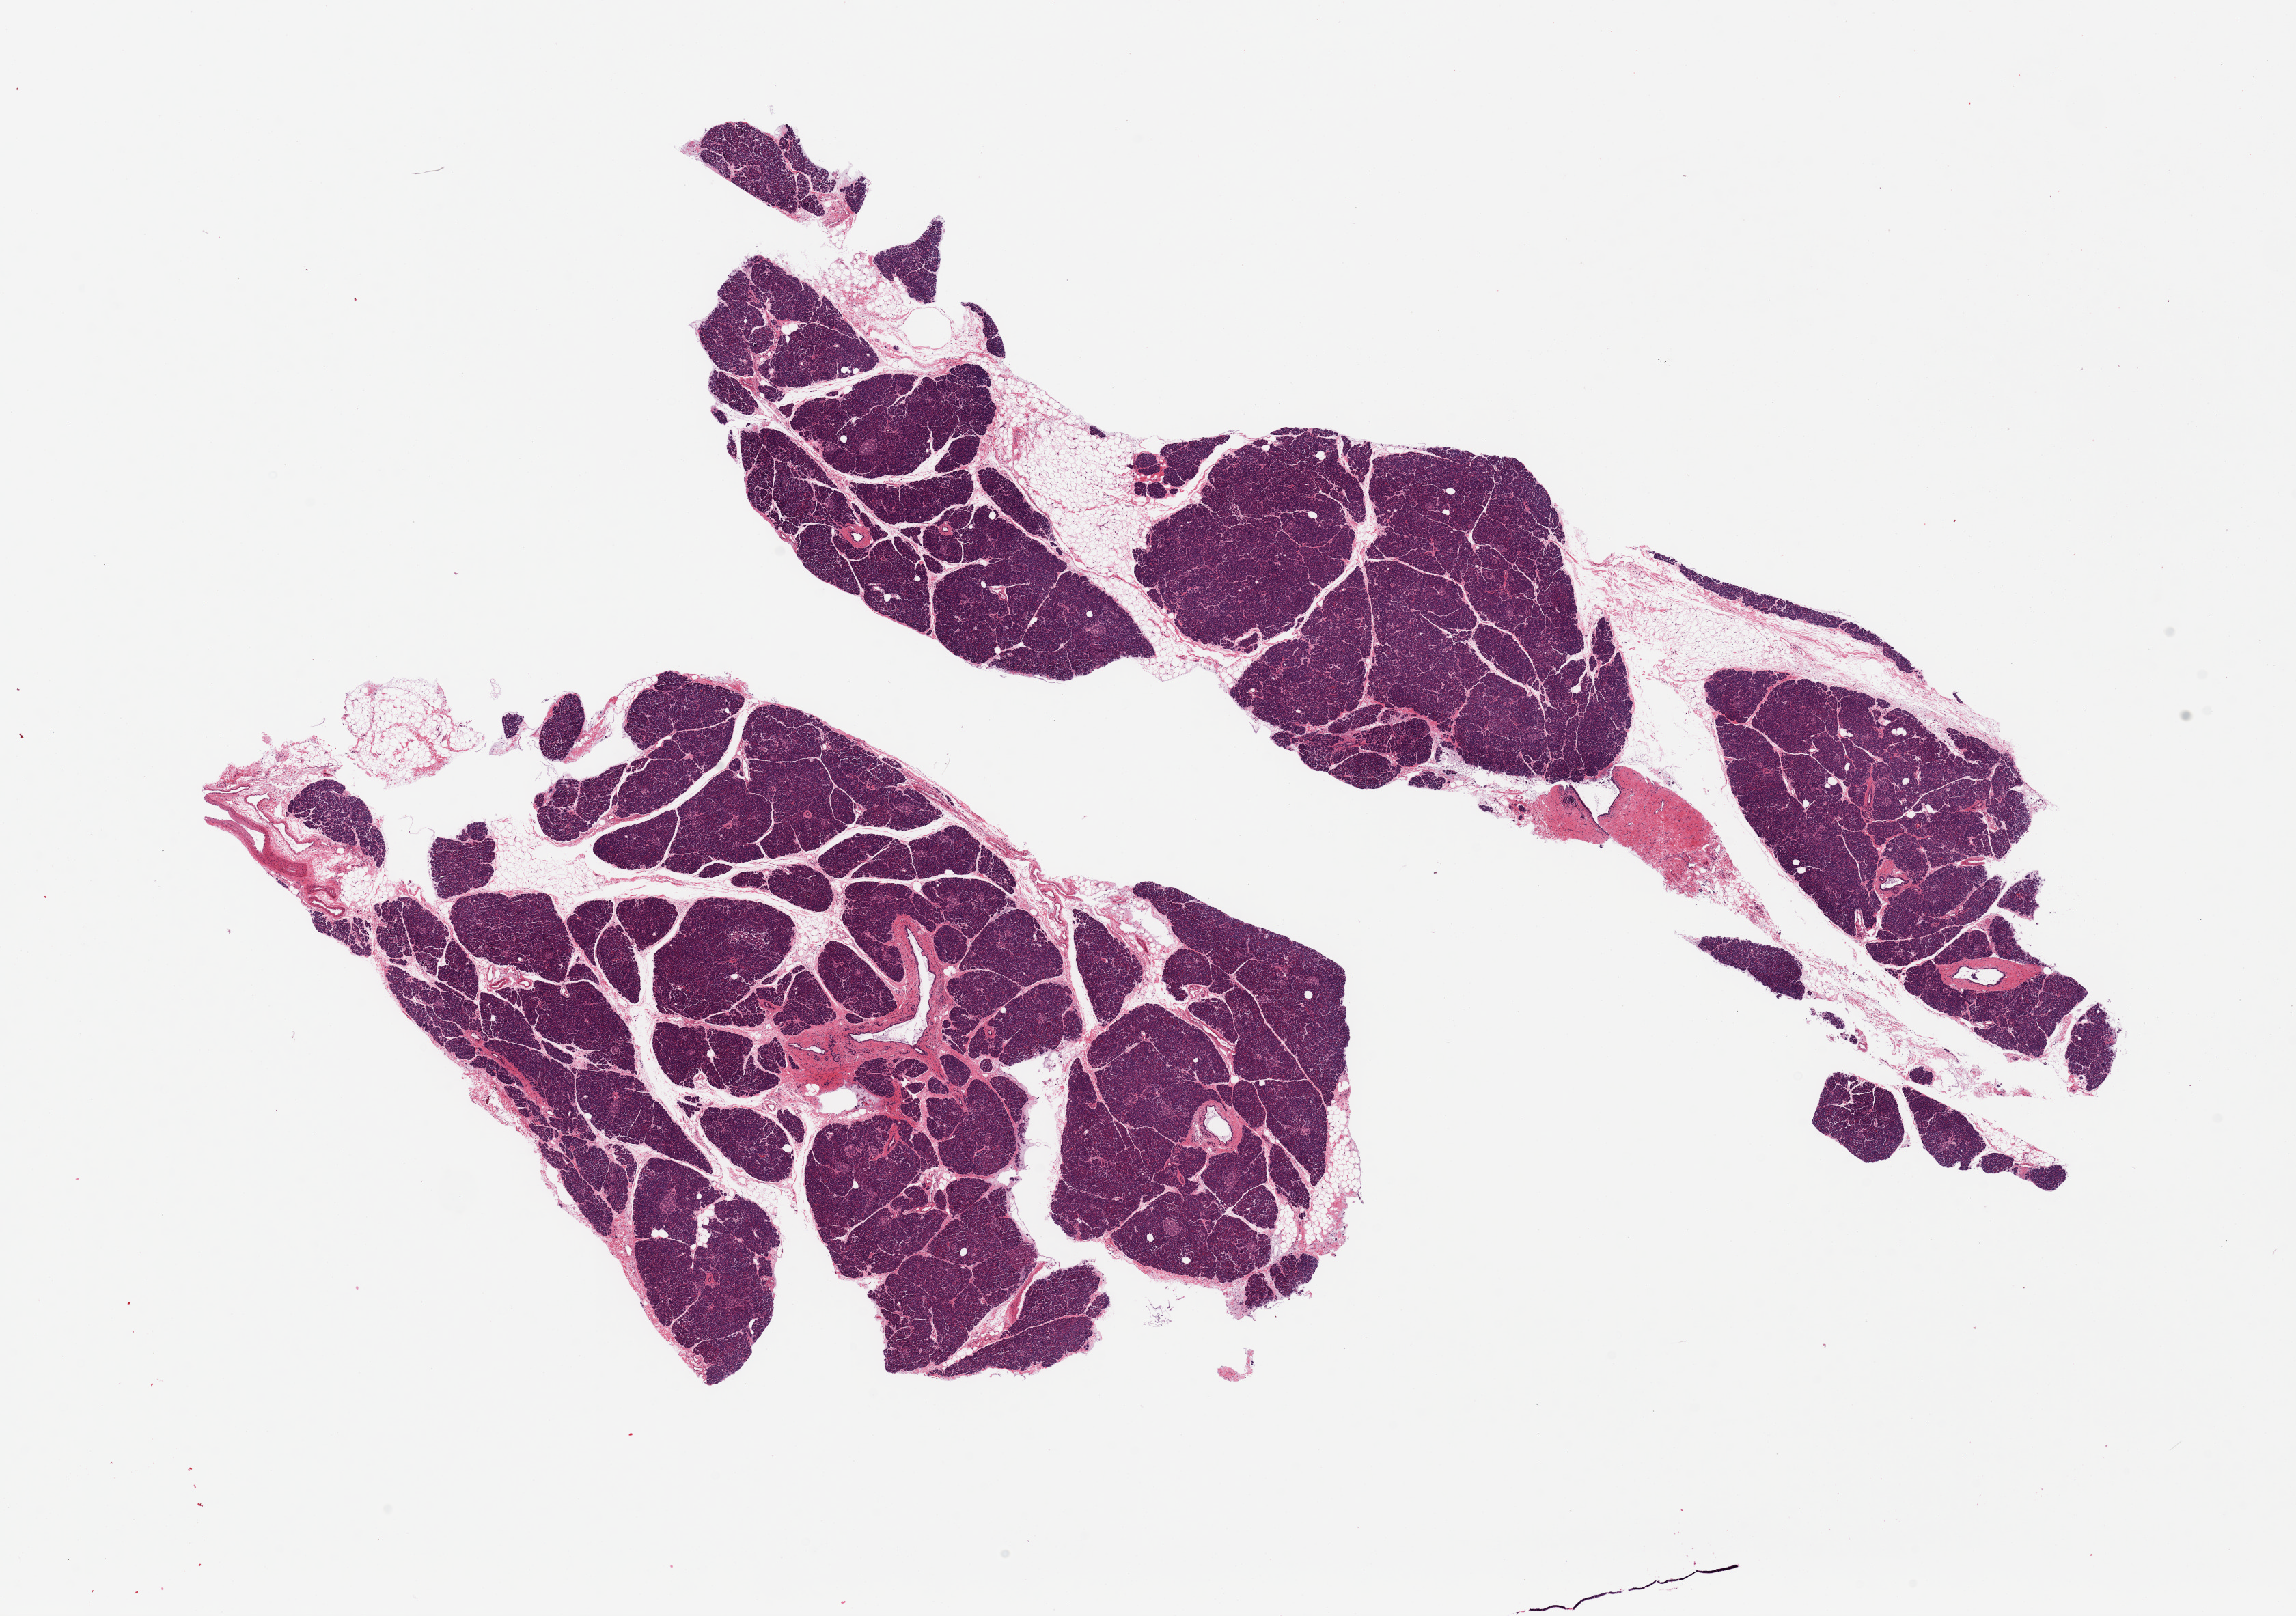
Digitized hematoxylin and eosin (H&E)-stained section, shown as a low-resolution overview of the whole scanned area (about 26.6 x 18.7 mm, slide scanned at 20x); PAXgene-fixed paraffin-embedded (PFPE) section; sampled site (target tissue): pancreas; donor tissue sample. Donor sex: female.
- reviewer comment on this tissue sample: 2 pieces ~20% interstitial fat; Islets well-visualized